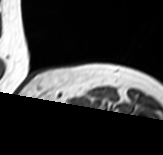
MRI of an extremity soft-tissue mass, one axial slice; slice 58 of 65 in the series (ordered by position); MR volume resampled by the dataset authors to the PET/CT grid (not the native acquisition matrix); 3.27 mm slice thickness; 163 × 155 image matrix. Female patient. Case-level facts recorded for this patient, not image findings: histological type: pleomorphic leiomyosarcoma; grade: high; site of the primary tumour: left thigh.
Annotated regions visible in this slice (expert contour drawn on MRI and transferred to this co-registered scan by the dataset authors):
- gross tumour volume including surrounding oedema: bounding box (x1, y1, x2, y2) in pixels: (46, 108, 61, 116)